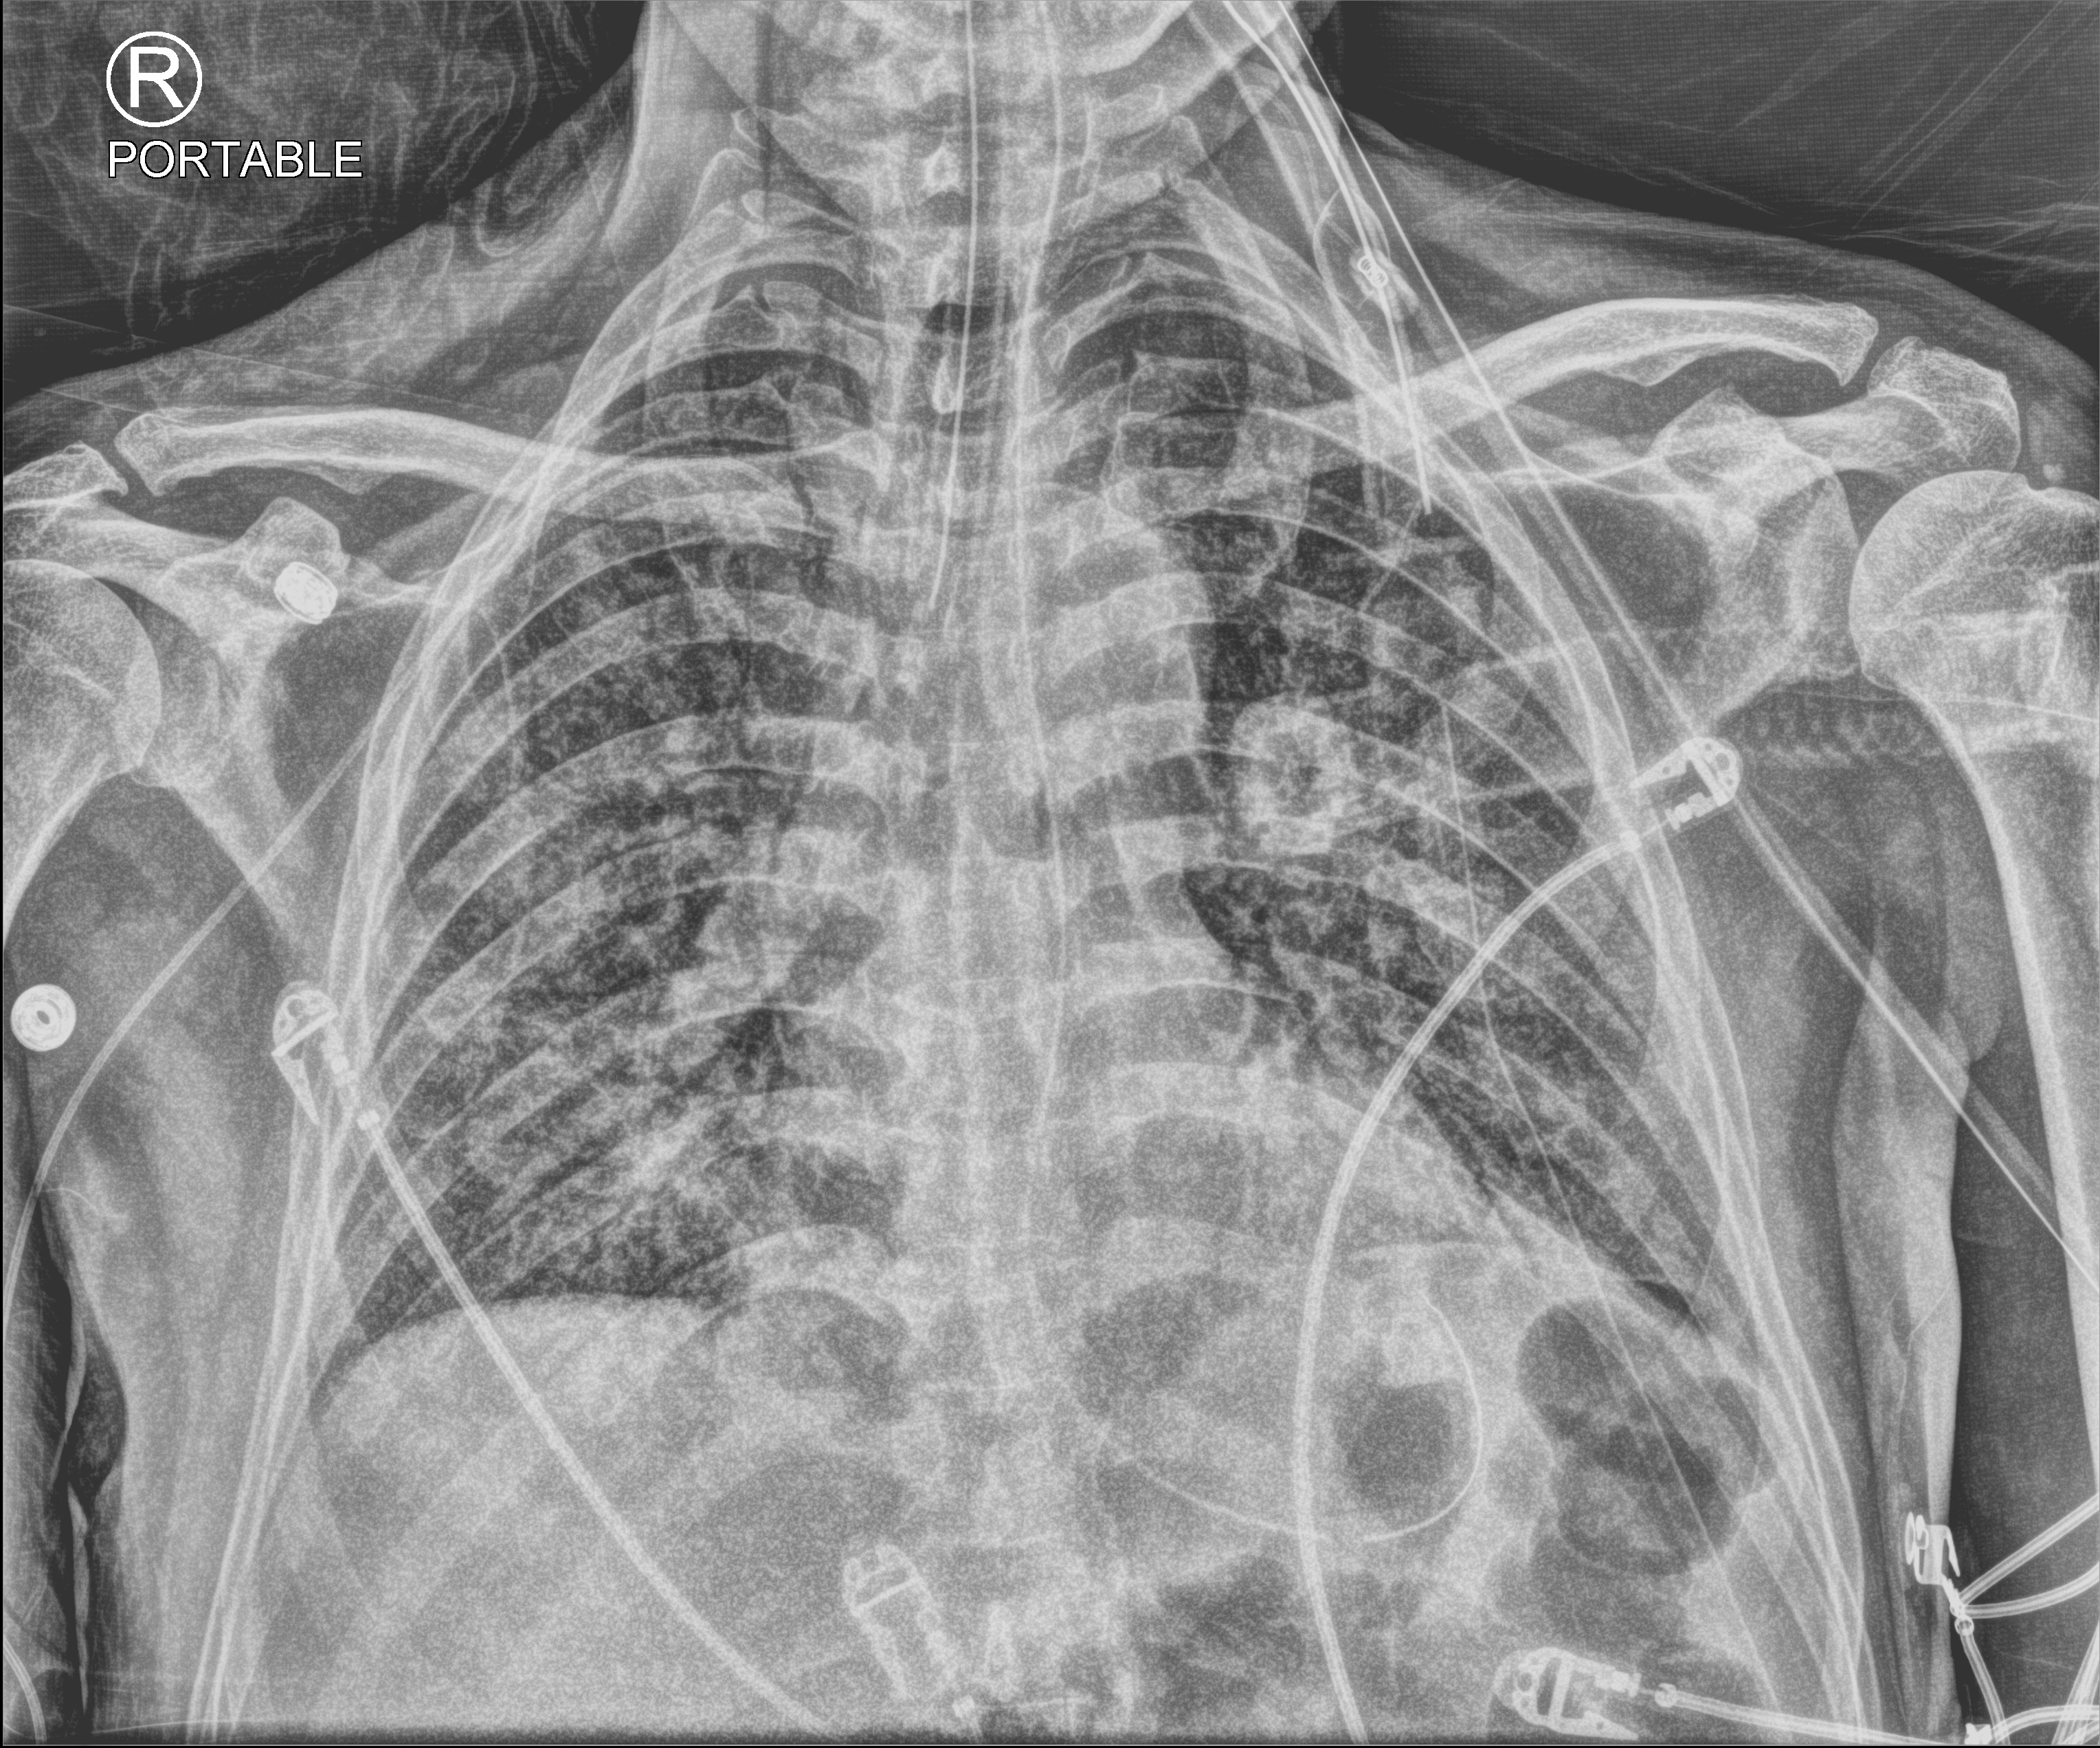
Bedside chest radiograph (computed radiography); anteroposterior (AP) projection. Male patient hospitalised with COVID-19, age 60–74 years.
From the hospital-stay record, not from the radiograph (when in the stay this image was taken is not recorded): mechanically ventilated during this hospital stay: yes; admitted to intensive care during this hospital stay: yes.